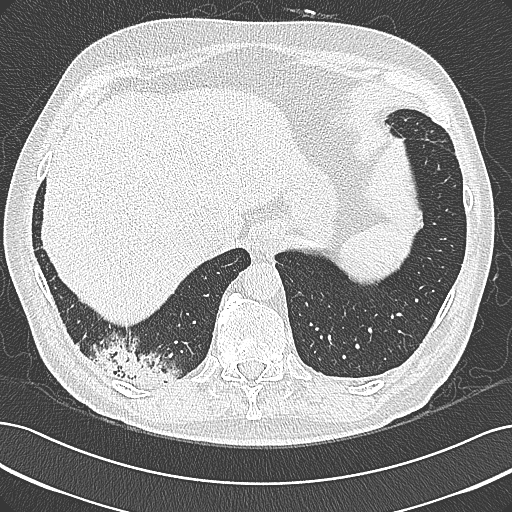
Chest CT (low-dose screening protocol), one axial image. First (baseline) screen. Lung window (W 1500 / L -600 HU). Lung (sharp) reconstruction kernel (B80f). Slice 247 of 355 in the series. 512 × 512 image matrix. Male, age 68 years at enrolment. Former smoker at enrolment.
Expert-annotated lung lesion, bounding box [x1, y1, x2, y2] px = [95, 338, 191, 399]. Screening reader's record for this exam: no non-calcified nodule ≥4 mm recorded. Official screen result: negative screen, significant abnormalities not suspicious for lung cancer. Later outcome: lung cancer diagnosed 154 days after this screen — mucinous adenocarcinoma, right lower lobe, well differentiated (G1), stage IB (AJCC 6th edition), 50 mm at pathology.